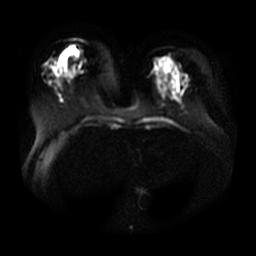
Breast MRI, one axial slice. Slice 11 of 29 in the series (ordered by position). Diffusion-weighted series; image 2 of 4 stored at this slice position (different b-values; order by instance number). 3 T. 5 mm slice thickness. 256 × 256 image matrix, field of view 380 × 380 mm. Female patient.
Annotated regions visible in this slice (expert manual segmentation):
- tumour on diffusion-weighted imaging: box from (x=67, y=50) to (x=70, y=53) px